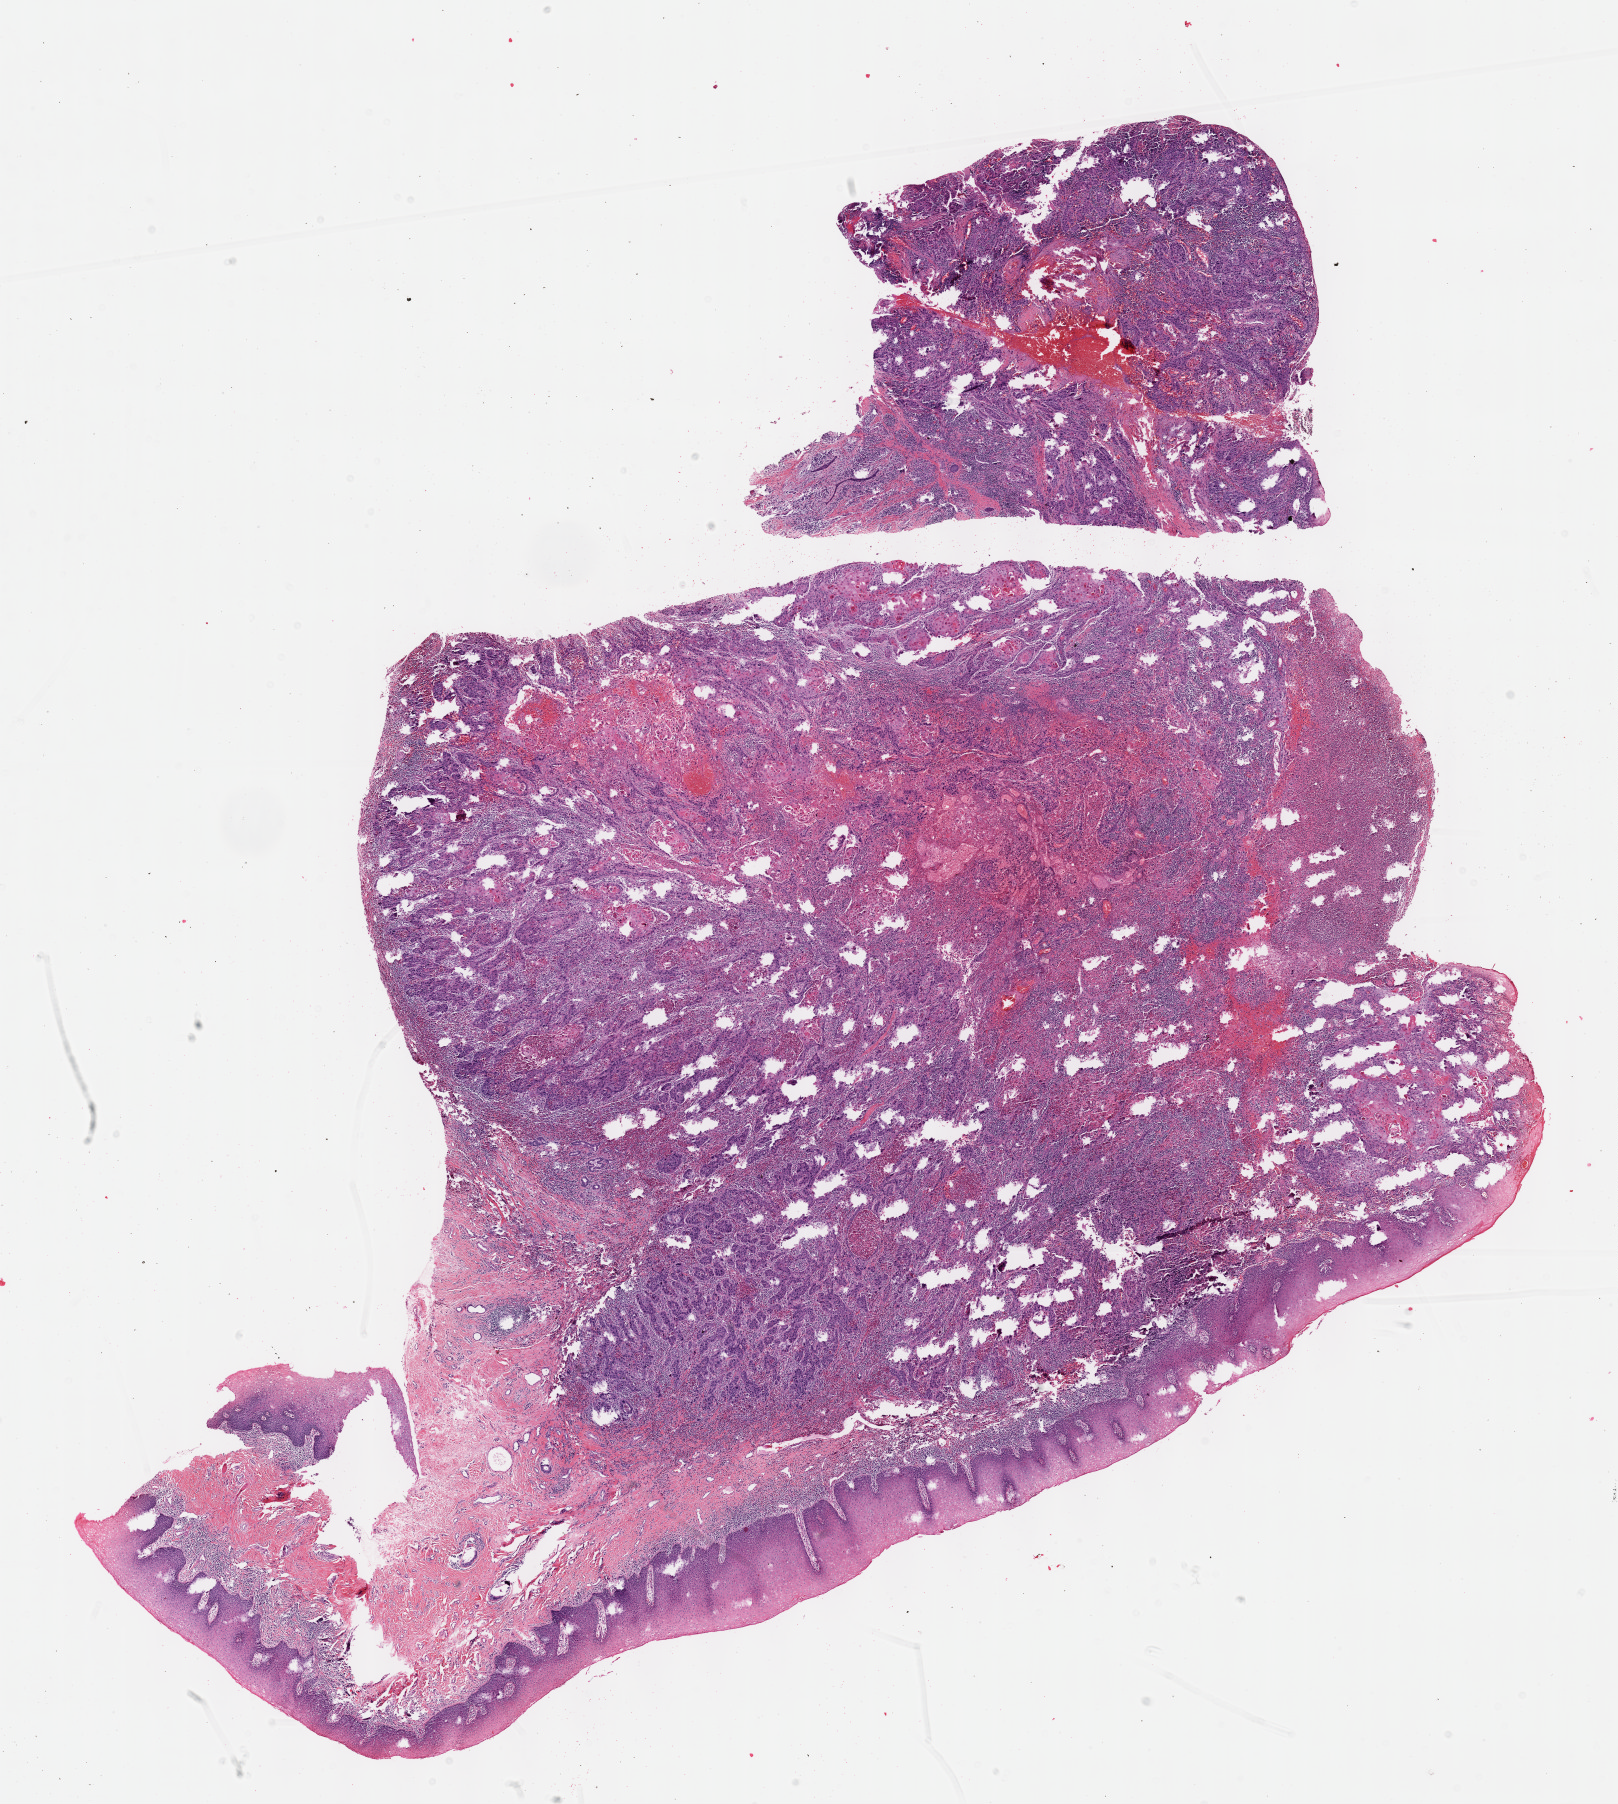
Whole-slide histology image, H&E-stained, low-resolution overview of the scanned area, about 13.1 x 14.6 mm. Formalin-fixed paraffin-embedded (FFPE) diagnostic section. Primary tumour sample from the head and neck. Female, age 73 years at initial diagnosis.
Pathologic diagnosis: Squamous cell carcinoma, NOS (overlapping lesion of lip, oral cavity and pharynx).